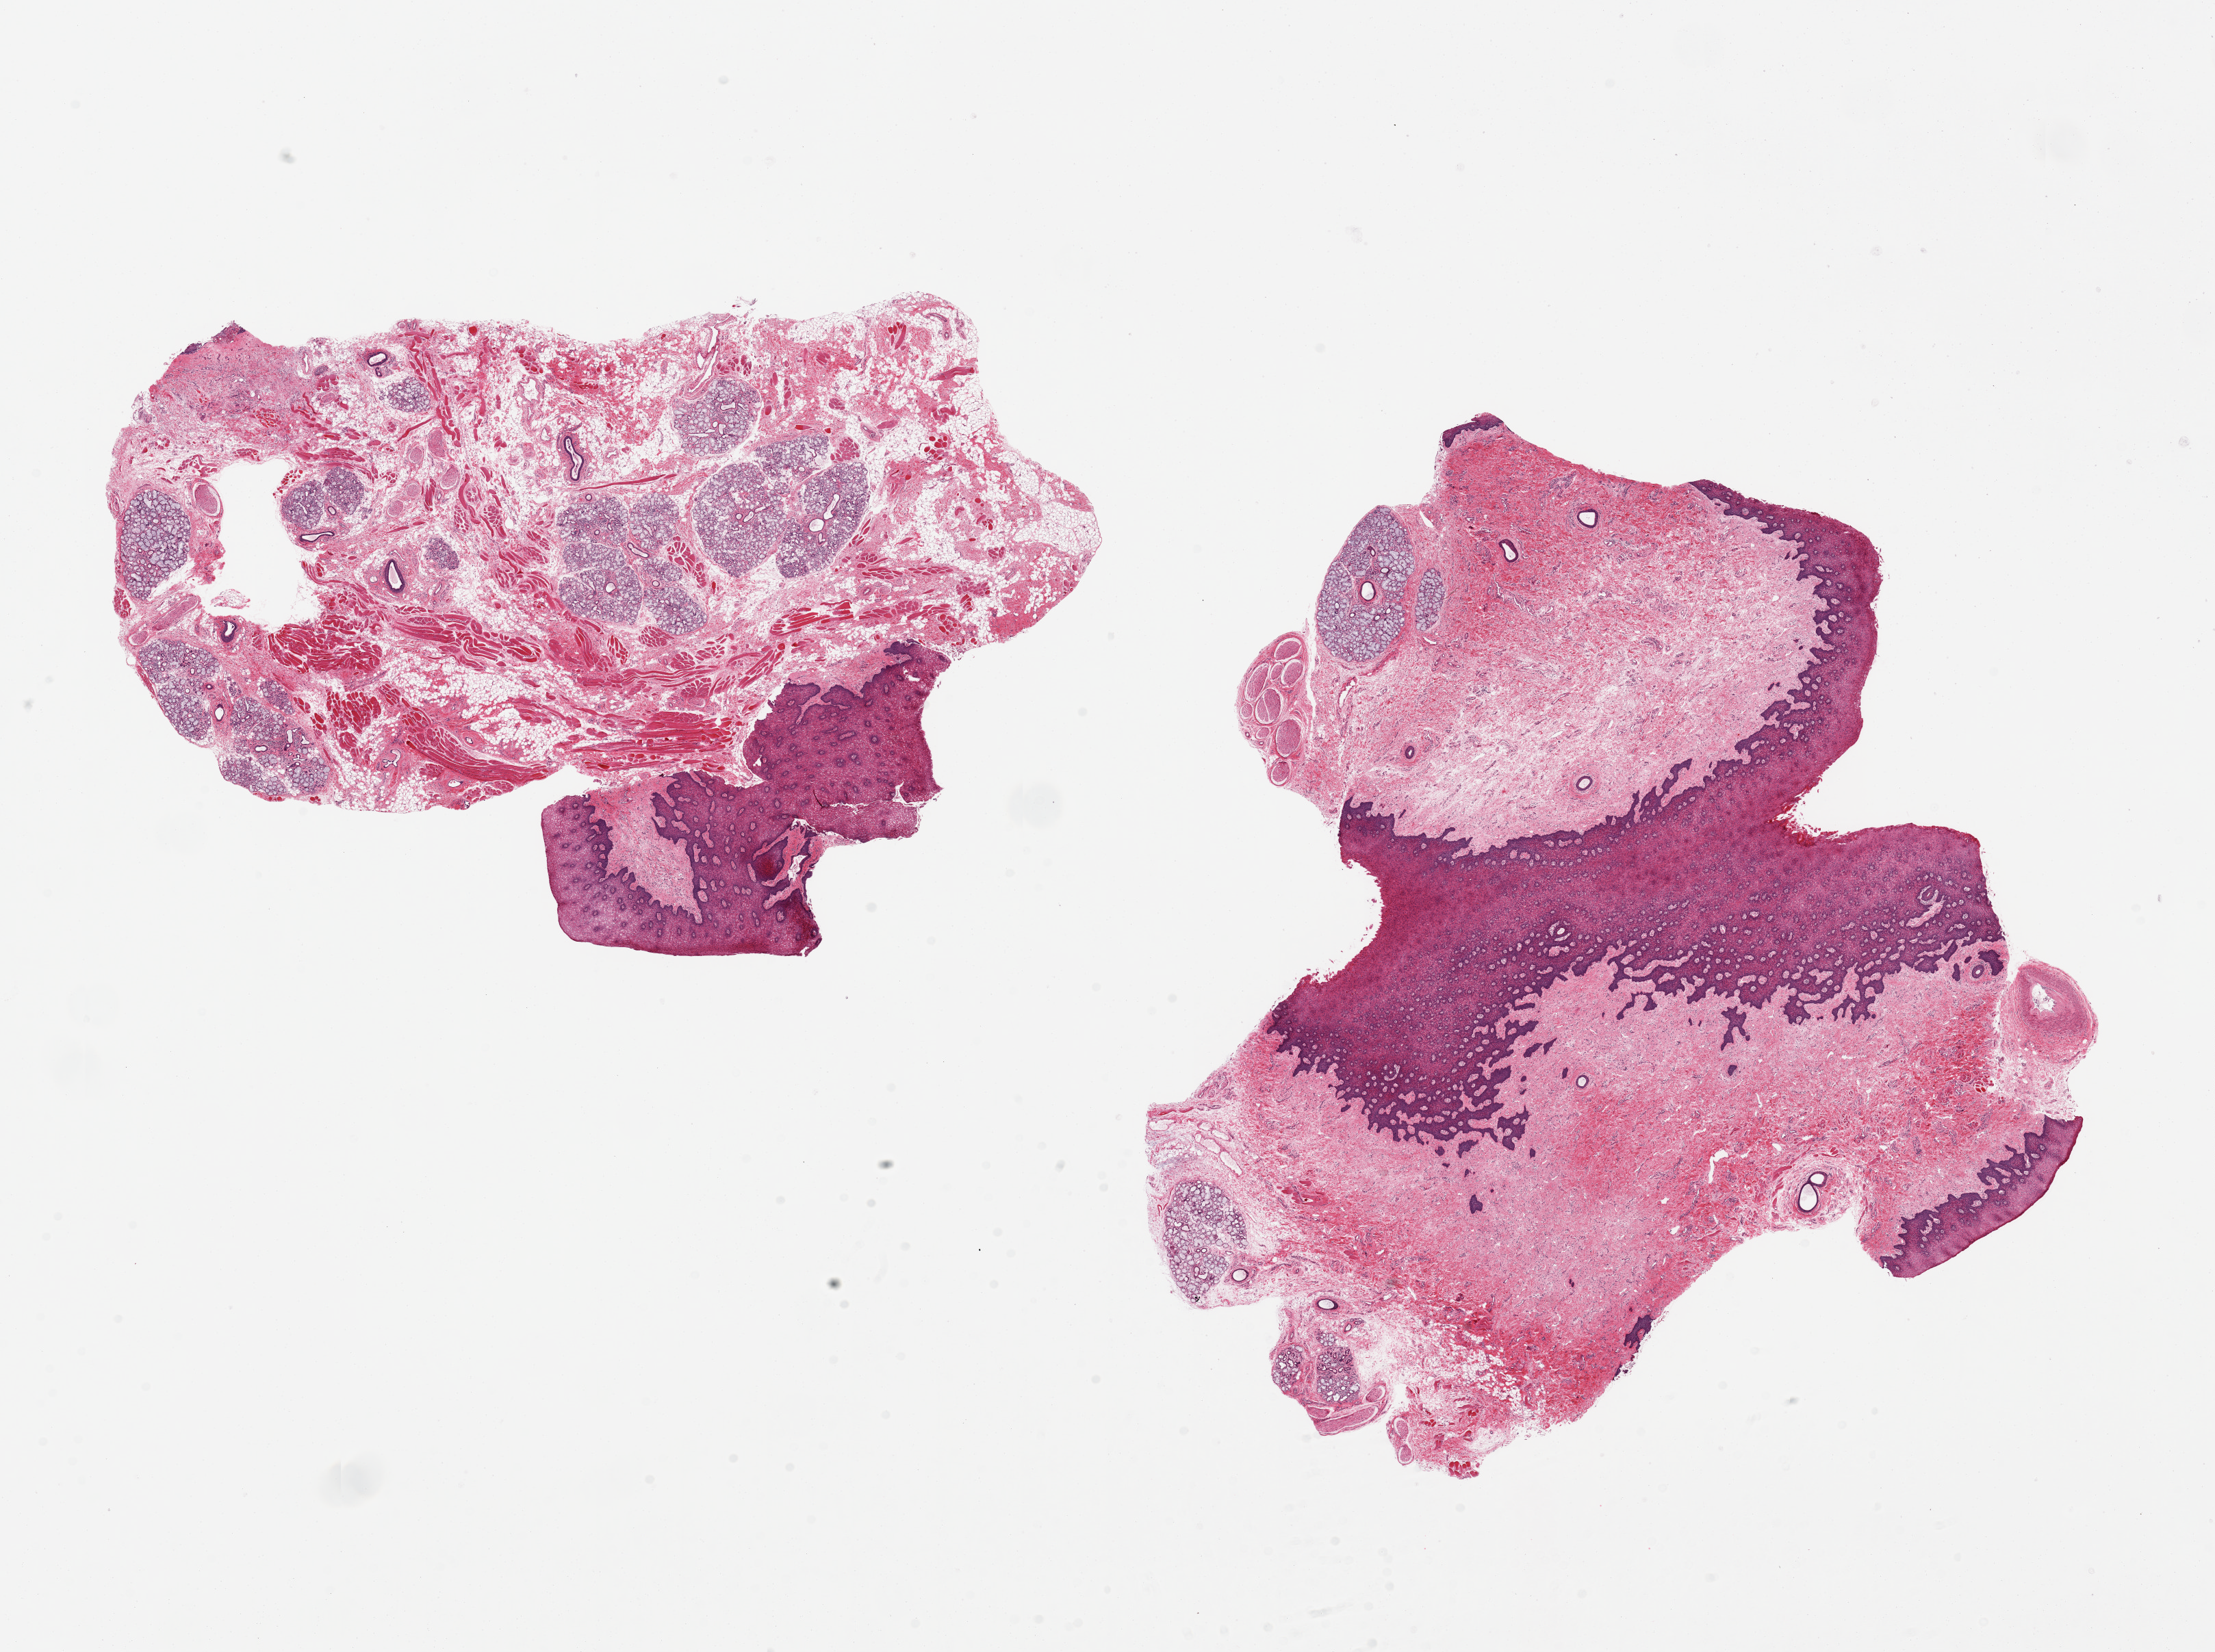
Digitized hematoxylin and eosin (H&E)-stained section — shown as a low-resolution overview of the whole scanned area (about 25.6 x 19.1 mm), PAXgene-fixed paraffin-embedded (PFPE) section, section of minor salivary gland (target tissue), tissue donor sample. Donor sex: female.
- reviewer comment on this tissue sample: 2 pieces; 11x9 & 12x11mm; 30% glands in 1, 10% in other; both good; Too much surface epithelium and fibrous stroma